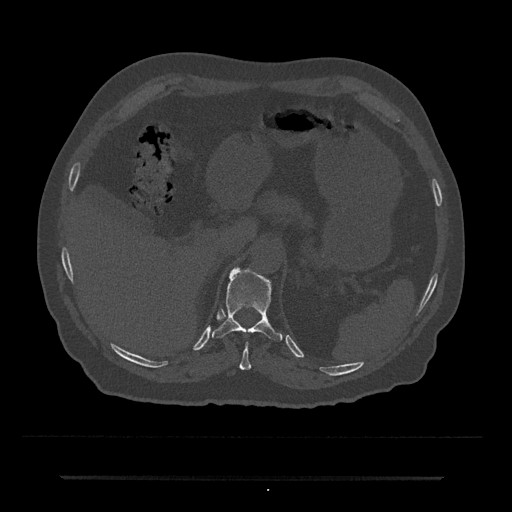
CT including the spine, one axial slice. Position 187 of 797 along the scan axis. 120 kVp. Bone window (W 1800 / L 400 HU). 0.5 mm slice thickness. 512 × 512 image matrix. Patient: male, 69 years. From the clinical record (not read from this slice): primary cancer: prostate.
Outlined on this slice (semi-automatically segmented with operator editing):
- T10 vertebra: bounding box [x1, y1, x2, y2] px = [239, 342, 251, 370]
- T11 vertebra: [212, 267, 283, 342]